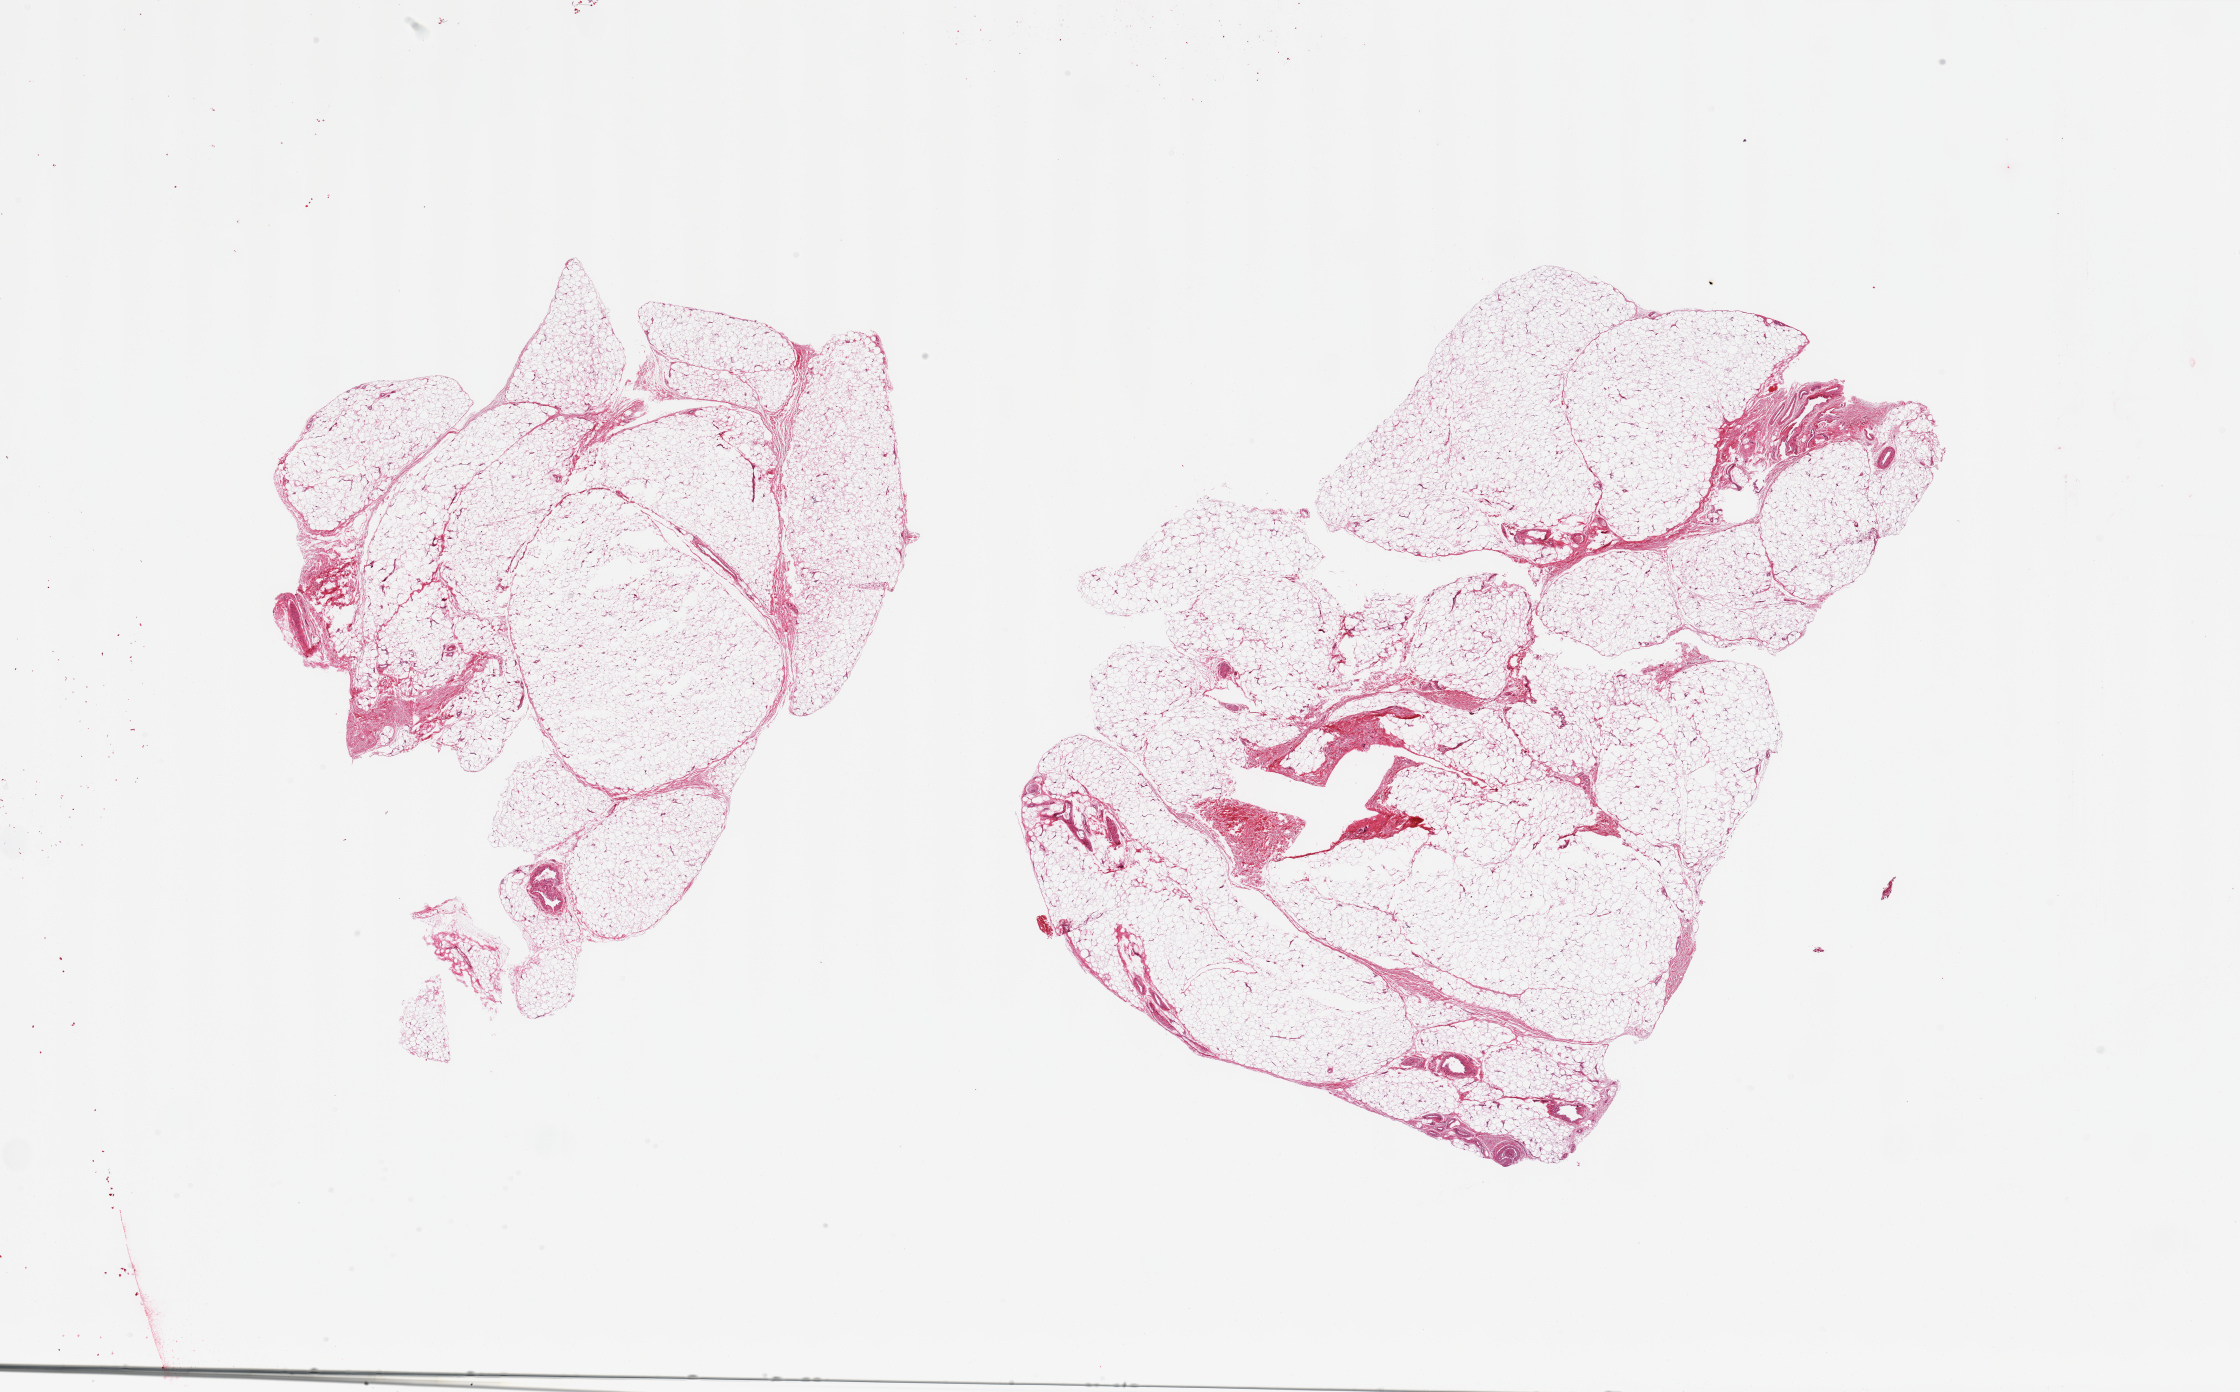
Digitized H&E-stained section, shown as a low-resolution overview of the whole scanned area (about 35.4 x 22.0 mm). PAXgene-fixed paraffin-embedded (PFPE) section. Section of adipose tissue (target tissue). Tissue donor sample. Male donor.
Review note (as recorded): 2 pieces; 5% fibrous content.